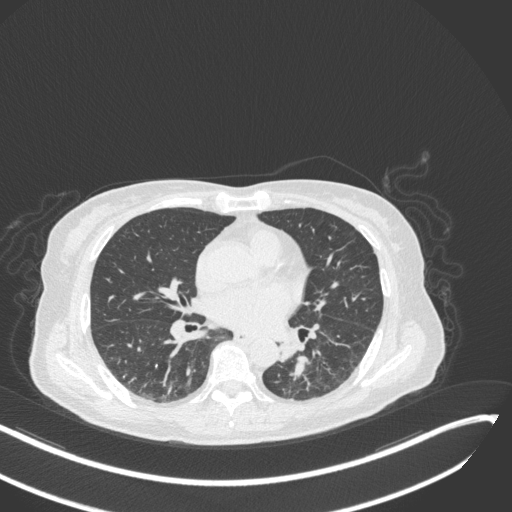
Chest CT, one axial slice; position 127 of 342 along the scan axis; 120 kVp; lung window (W 1500 / L -600 HU); 1 mm slice thickness; 512 × 512 image matrix. Patient: female, 64 years. From the clinical record (not read from this slice): clinical TNM (as recorded): T3 N1 M1; histopathological grade: G3.
Annotated regions visible in this slice (bounding box drawn by a radiologist):
- lung tumour (recorded histology: small cell carcinoma): bounding box <278,336,309,378> (left, top, right, bottom; pixels)